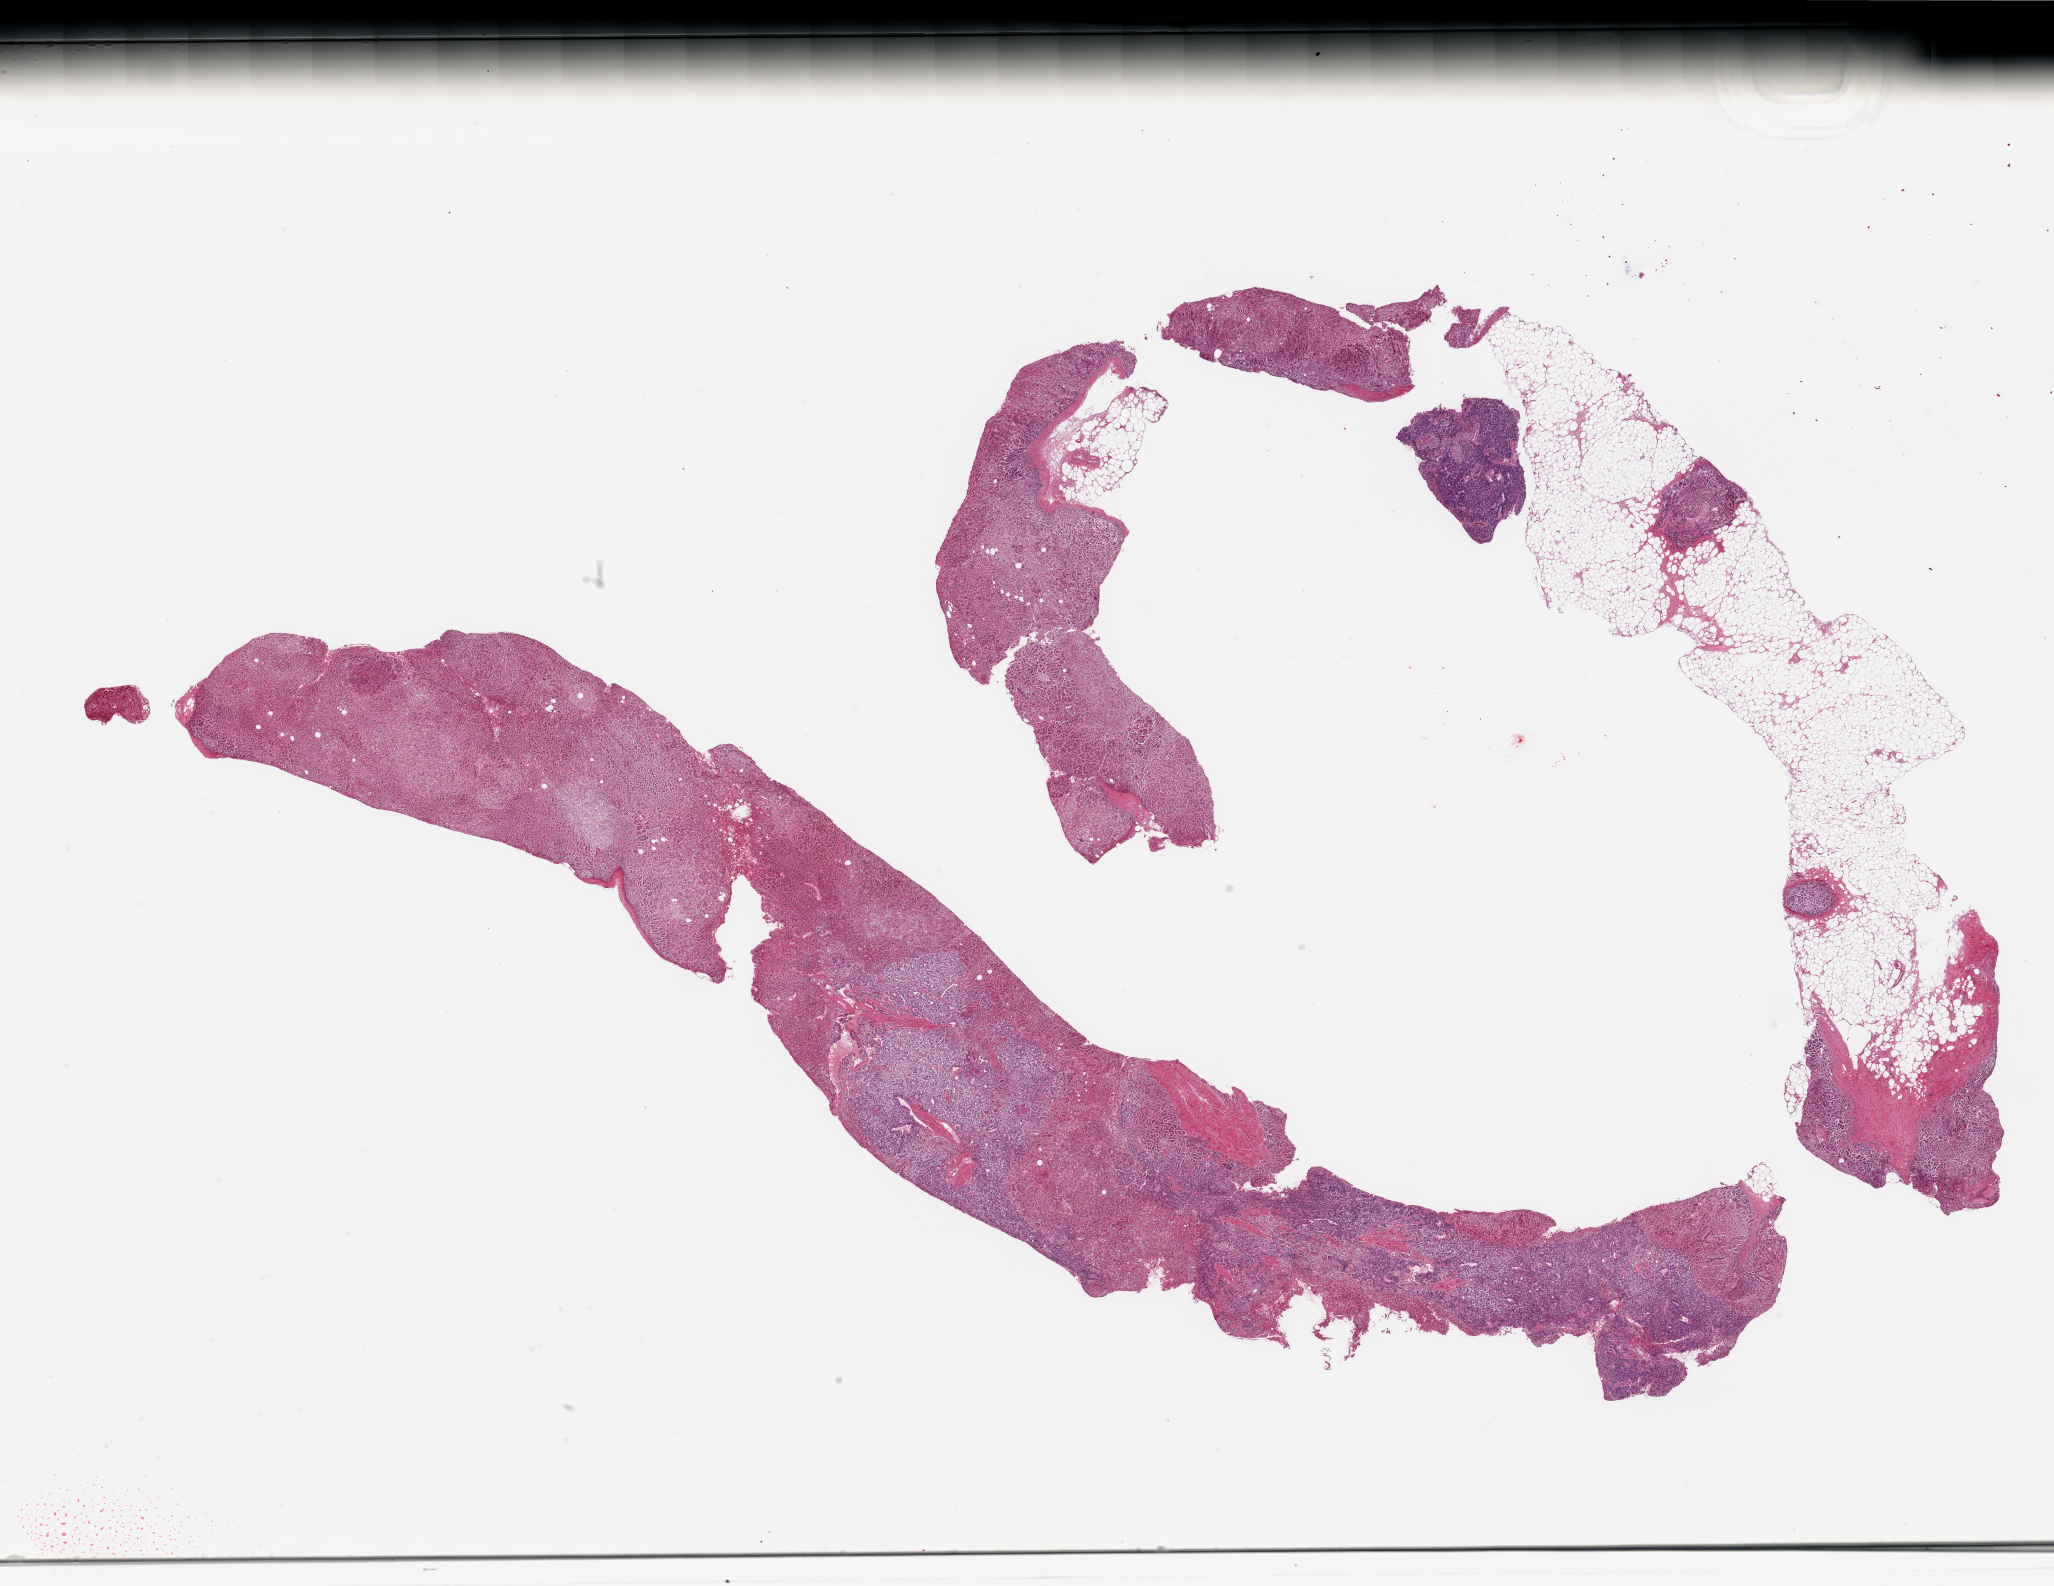
Whole-slide image, hematoxylin and eosin (H&E) stain — shown as a low-resolution overview of the whole scanned area (about 32.5 x 25.1 mm); PAXgene-fixed paraffin-embedded (PFPE) section; section of adrenal gland (target tissue); donor tissue sample. Donor sex: male.
Review note (as recorded): 2 pieces (fragmented): mainly cortex, 2 mm fragment of medulla; moderate-severe autolysis.